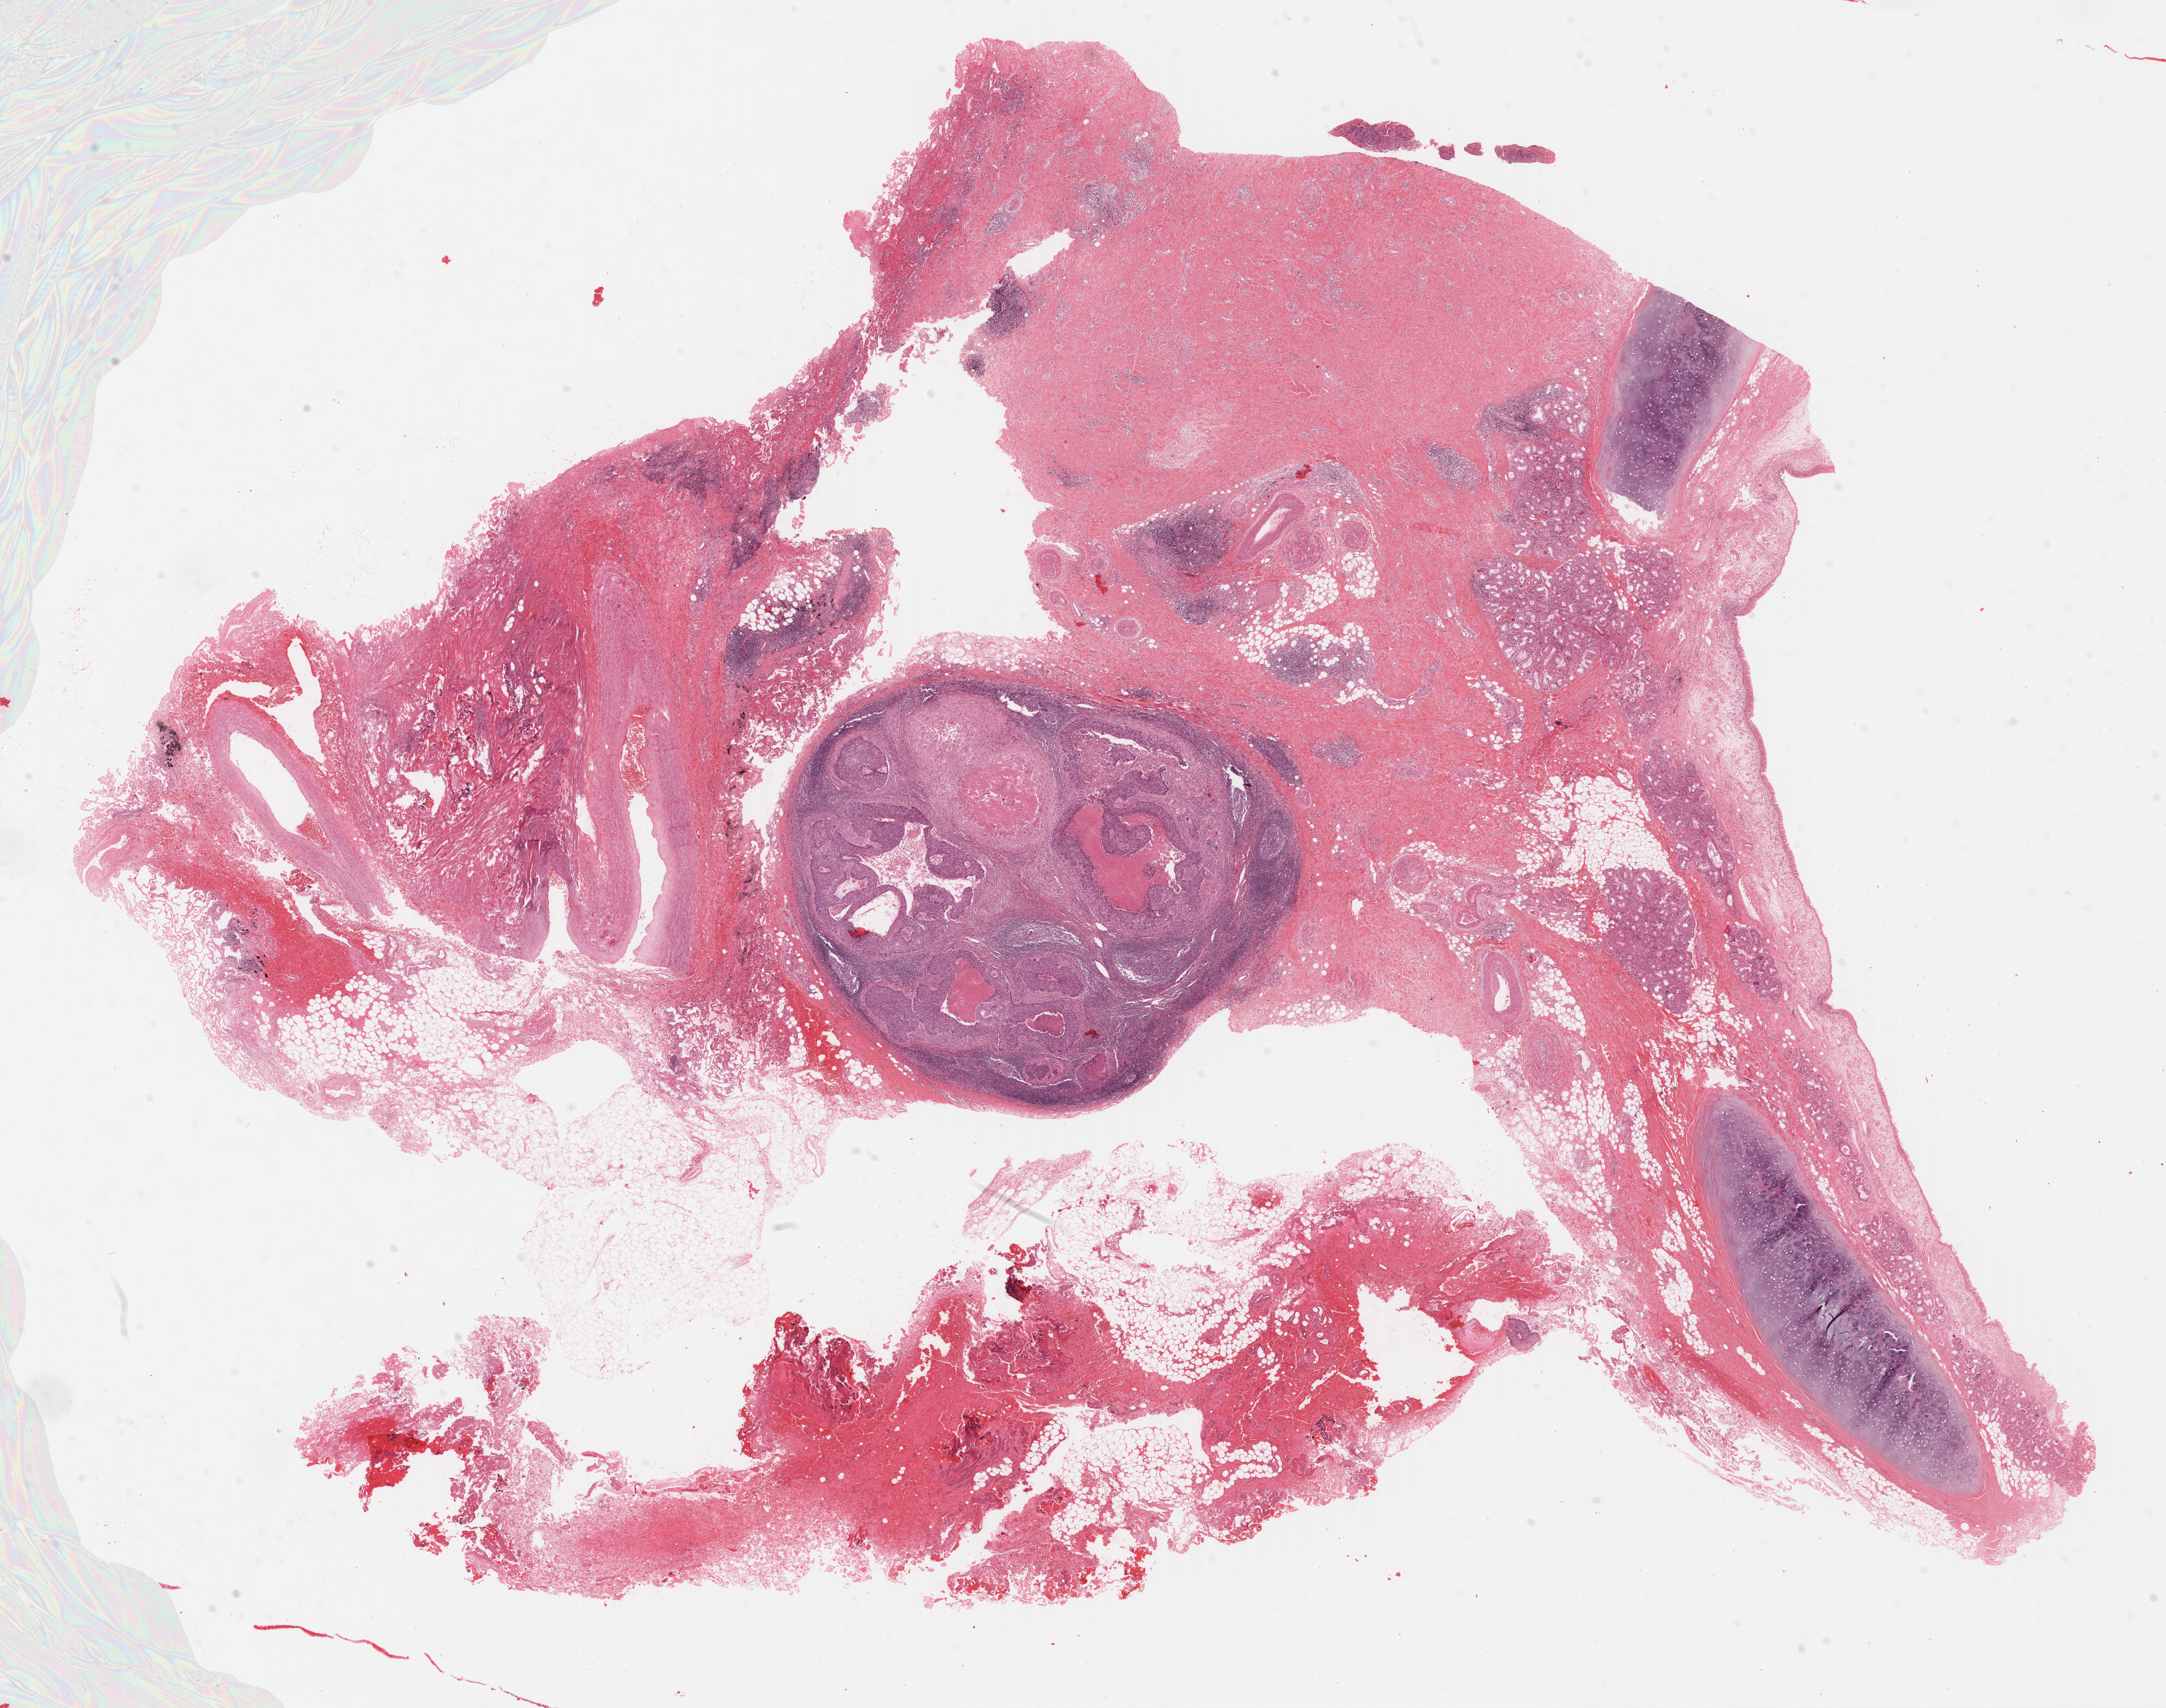
Hematoxylin and eosin (H&E) stained whole-slide image, low-resolution overview of the scanned area, about 23.4 x 18.4 mm. Formalin-fixed paraffin-embedded (FFPE) diagnostic section. Primary tumour sample from the lung. Male, age 63 years at initial diagnosis.
AJCC pathologic stage: IIB (6th edition). Pathologic diagnosis: Squamous cell carcinoma, NOS (upper lobe, lung).